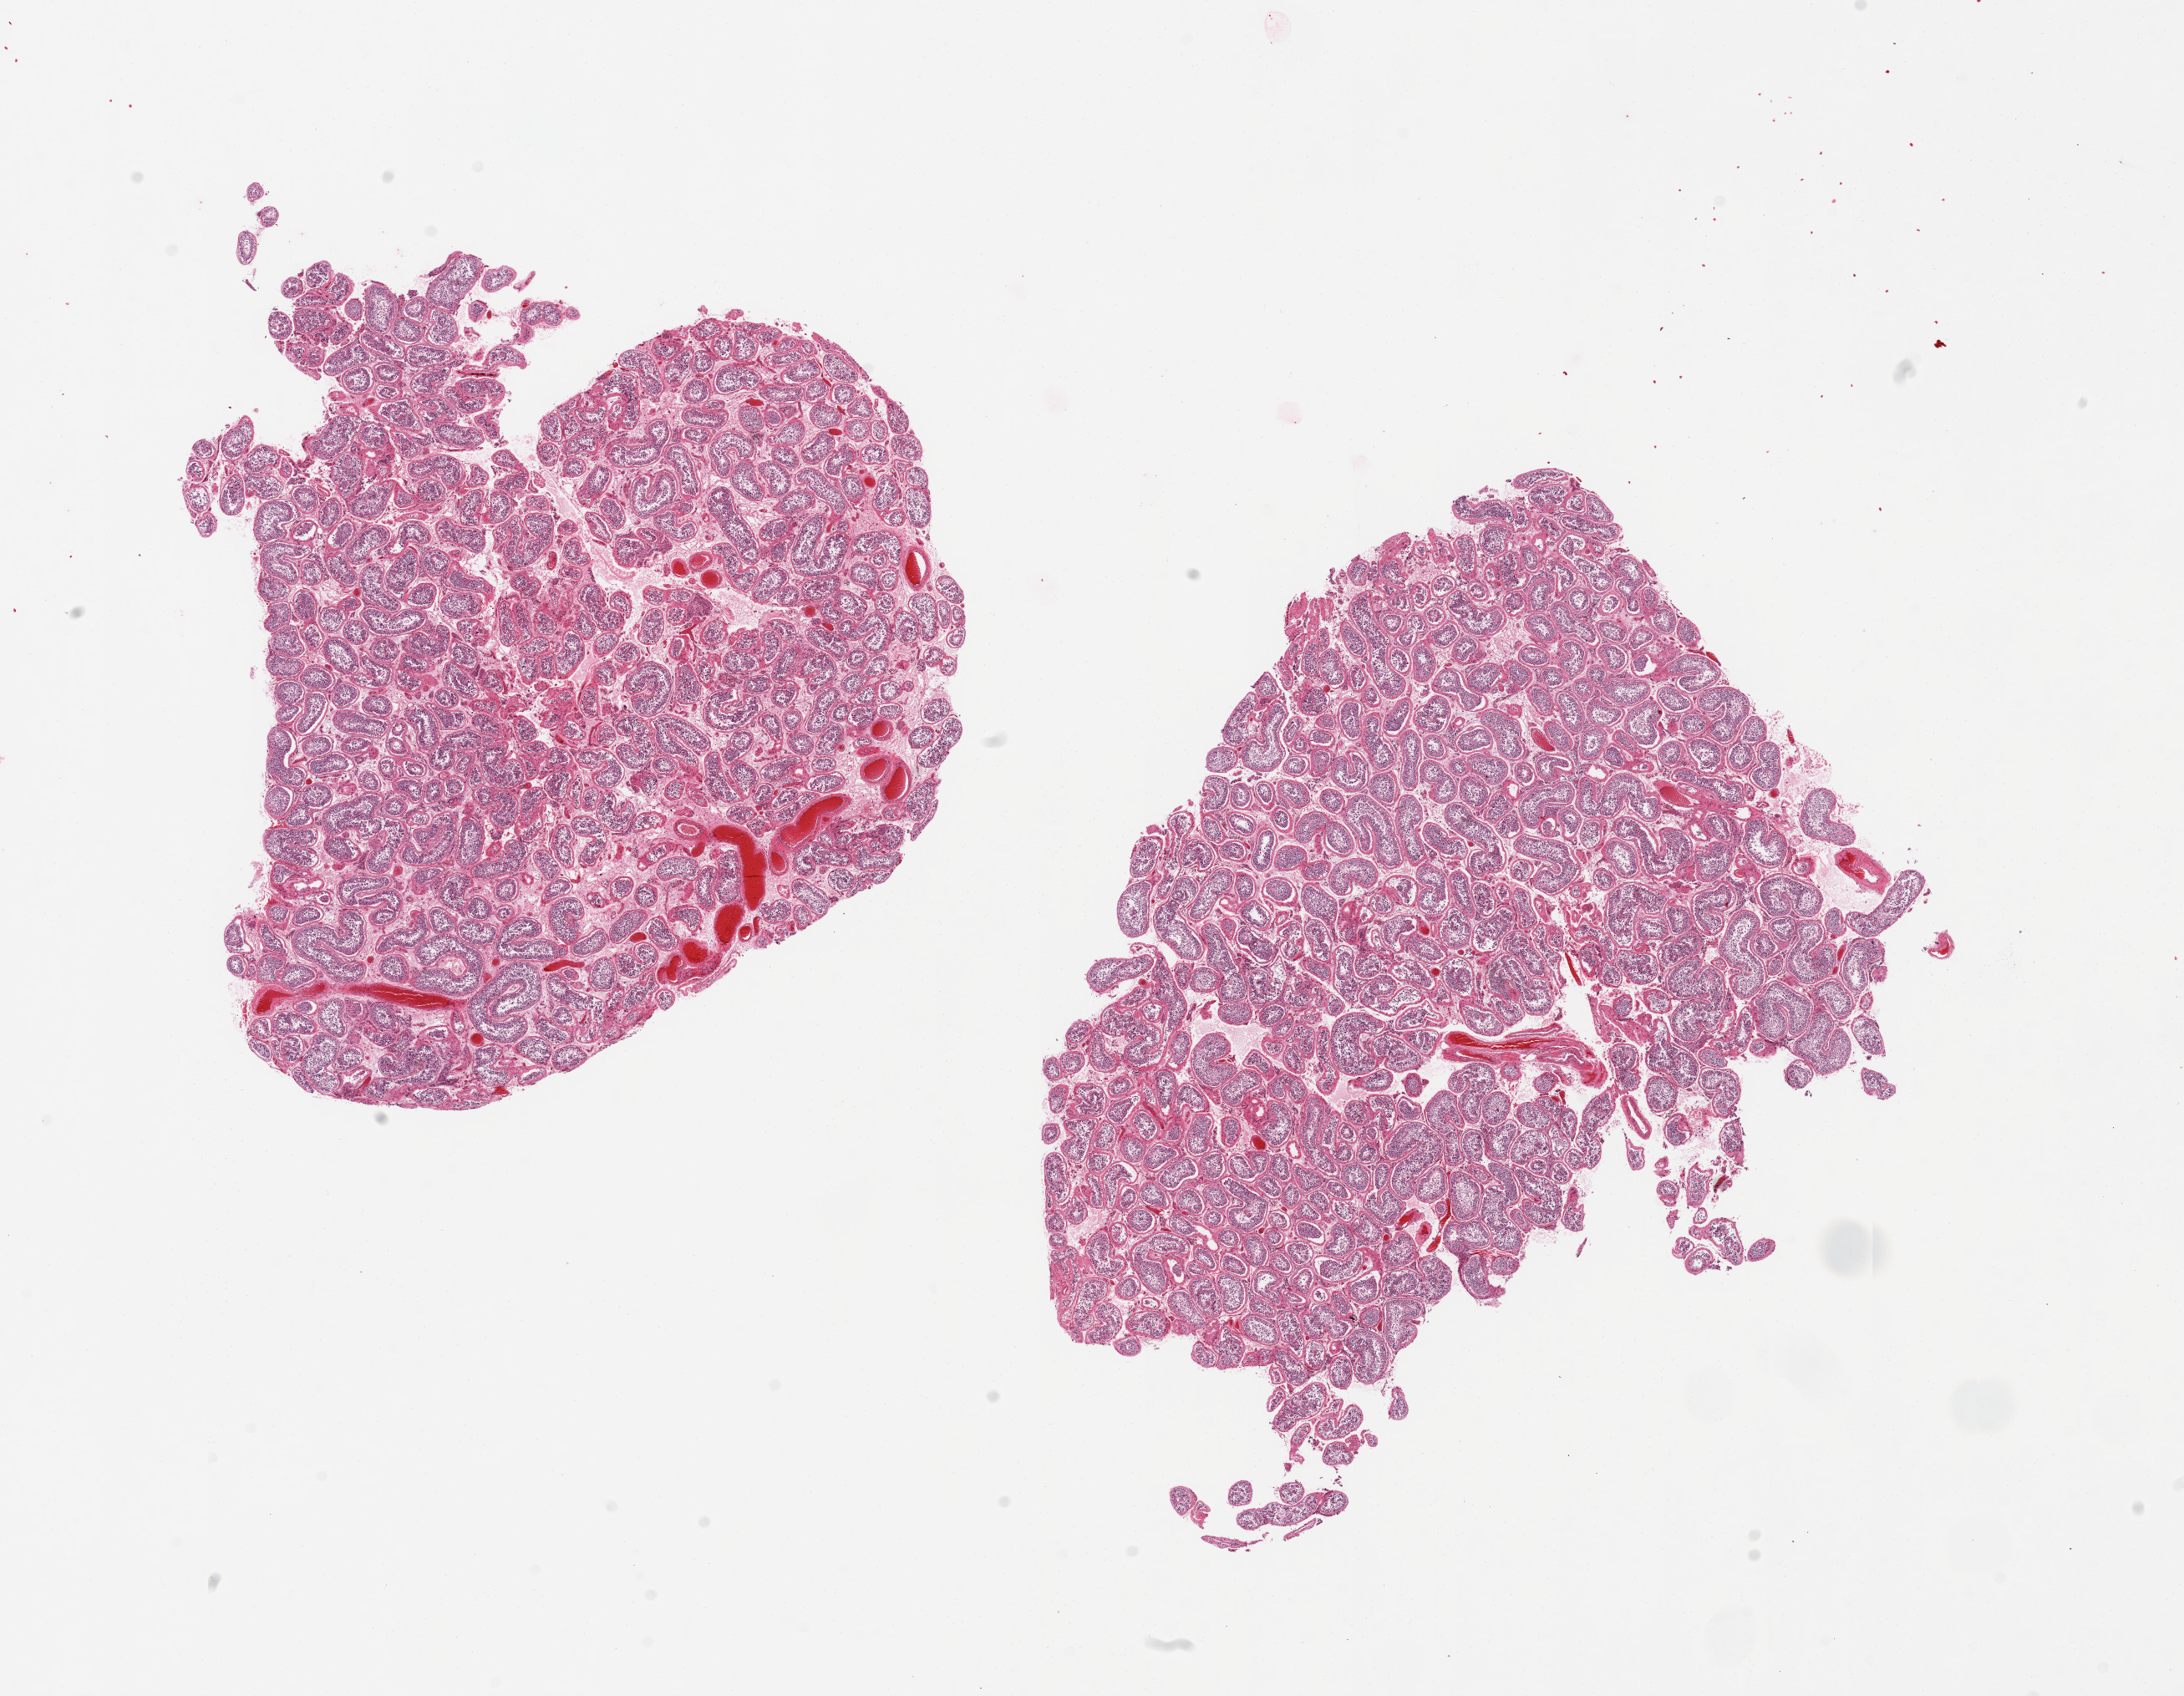
Haematoxylin and eosin whole-slide image, shown as a low-resolution overview of the whole scanned area (about 20.7 x 16.1 mm). PAXgene-fixed paraffin-embedded (PFPE) section. Sampled site (target tissue): testis. Tissue donor sample. Male donor.
• pathologist's review note for this sample: 2 pieces, spermatogenesis is present, markedly autolyzed